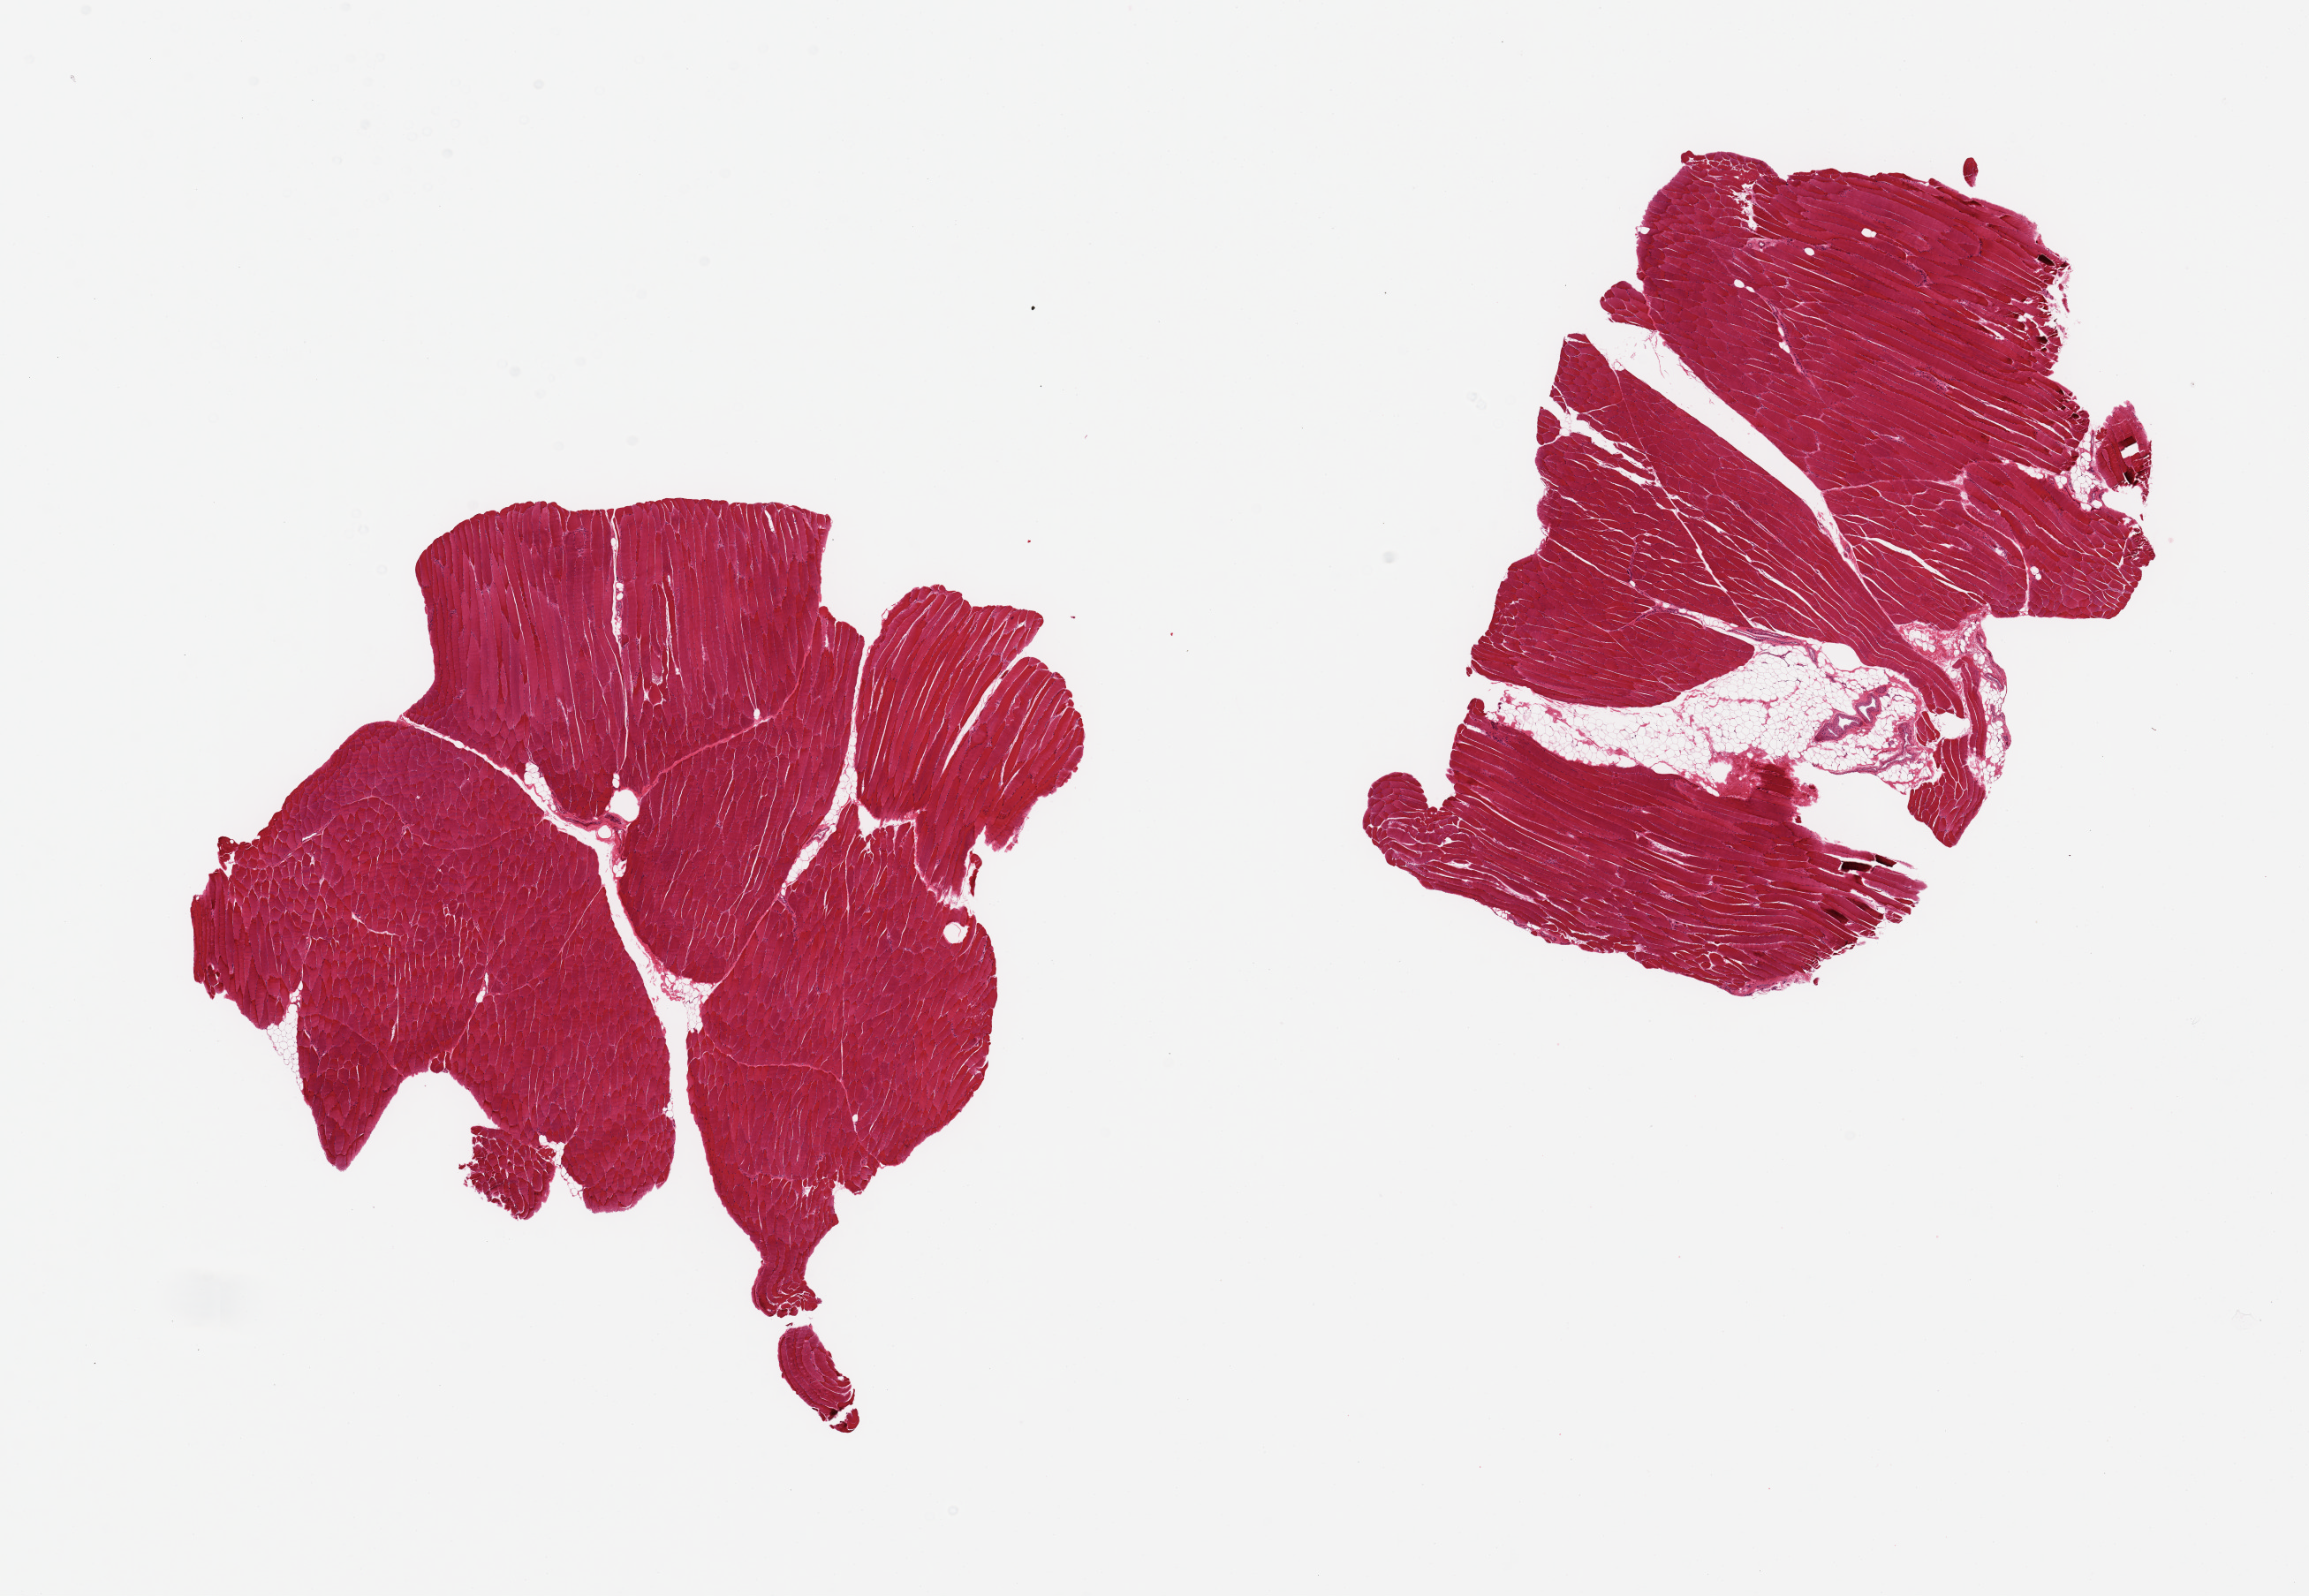
Digitized H&E-stained section — a low-resolution overview of the entire scanned area, about 20.7 x 14.3 mm (slide scanned at 20x); PAXgene-fixed paraffin-embedded (PFPE) section; section of skeletal muscle (target tissue); tissue donor sample. Donor: female.
Pathologist's review note for this sample: 2 pieces; 1 piece includes ~10% internal fat.